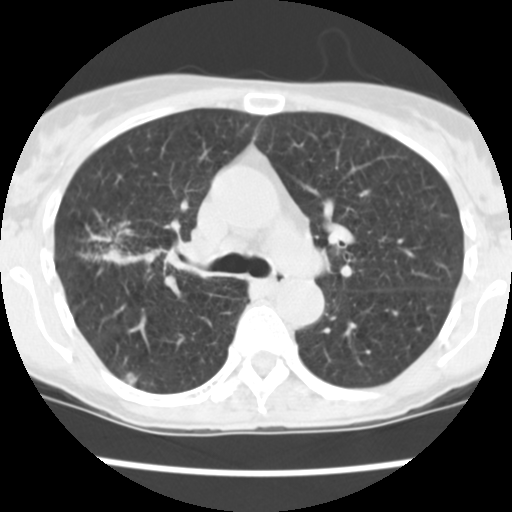
Low-dose screening chest CT, one axial slice; position 159 of 252 along the scan axis; lung window (W 1500 / L -600 HU); 2.5 mm slice thickness; 512 × 512 image matrix, field of view 276 × 276 mm.
Structures marked on this image (outlined manually by an expert reader):
- lesion 1 (tumor, upper lobe of right lung): bounding box [x1, y1, x2, y2] px = [125, 373, 137, 384]
- lesion 2 (tumor, lower lobe of right lung): [95, 245, 142, 265]